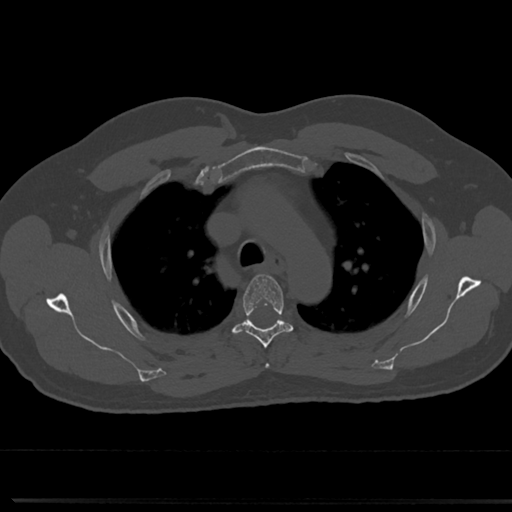
CT including the spine, one axial slice; position 547 of 817 along the scan axis; reconstruction kernel Br40s/3; 120 kVp; bone window (W 1800 / L 400 HU); 0.5 mm slice thickness; 512 × 512 image matrix, field of view 355 × 355 mm. Male patient, age 61 years. Case-level facts recorded for this patient, not image findings: primary cancer: prostate.
Annotated regions visible in this slice (semi-automatically segmented with operator editing):
- T3 vertebra: box from (x=265, y=363) to (x=269, y=368) px
- T4 vertebra: (x=232, y=274)–(x=295, y=347)